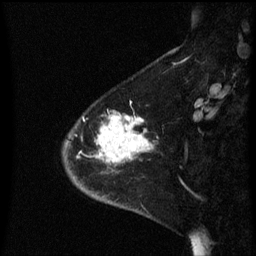
Breast MRI (dynamic contrast-enhanced), one sagittal slice. Slice 18 of 60 in the series (ordered by position). Dynamic contrast-enhanced series, image 2 of 3 at this slice position (ordered by acquisition). 1.5 T. TE 4.2 ms, TR 8.4 ms. 2.3 mm slice thickness. 256 × 256 image matrix. Female patient, age 46 years. Case-level facts recorded for this patient, not image findings: setting: breast cancer imaged before/during neoadjuvant chemotherapy; receptor status: HER2-positive.
Structures marked on this image (semi-automatically segmented with operator editing):
- analysis volume of interest (the breast-tissue region the enhancement analysis was run in; not a lesion): box from (x=63, y=110) to (x=157, y=187) px
- tumour enhancement mask (voxels above the 70 % enhancement threshold inside the analysis volume of interest): (x=95, y=112)–(x=153, y=163)